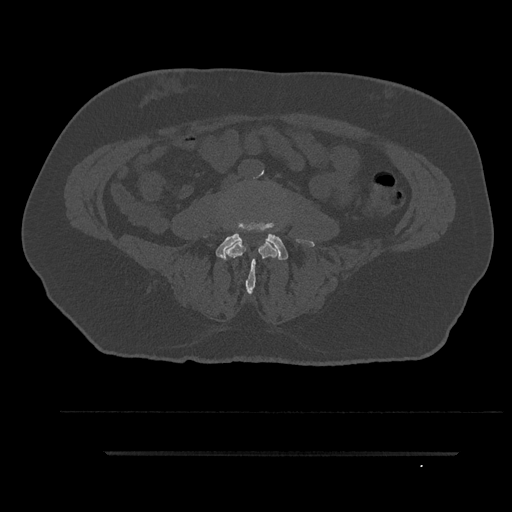
CT including the spine, one axial slice; slice 1 of 797 in the series (ordered by position); reconstruction kernel Br40s/3; 120 kVp; bone window (W 1800 / L 400 HU); 512 × 512 image matrix. Male patient, age 63 years. Case-level facts recorded for this patient, not image findings: primary cancer: renal; vertebrae with lytic lesions (as recorded): T8.
Outlined on this slice (semi-automatic segmentation, software-assisted and operator-edited):
- L3 vertebra: bounding box <226,240,277,292> (left, top, right, bottom; pixels)
- L4 vertebra: <216,233,288,260>